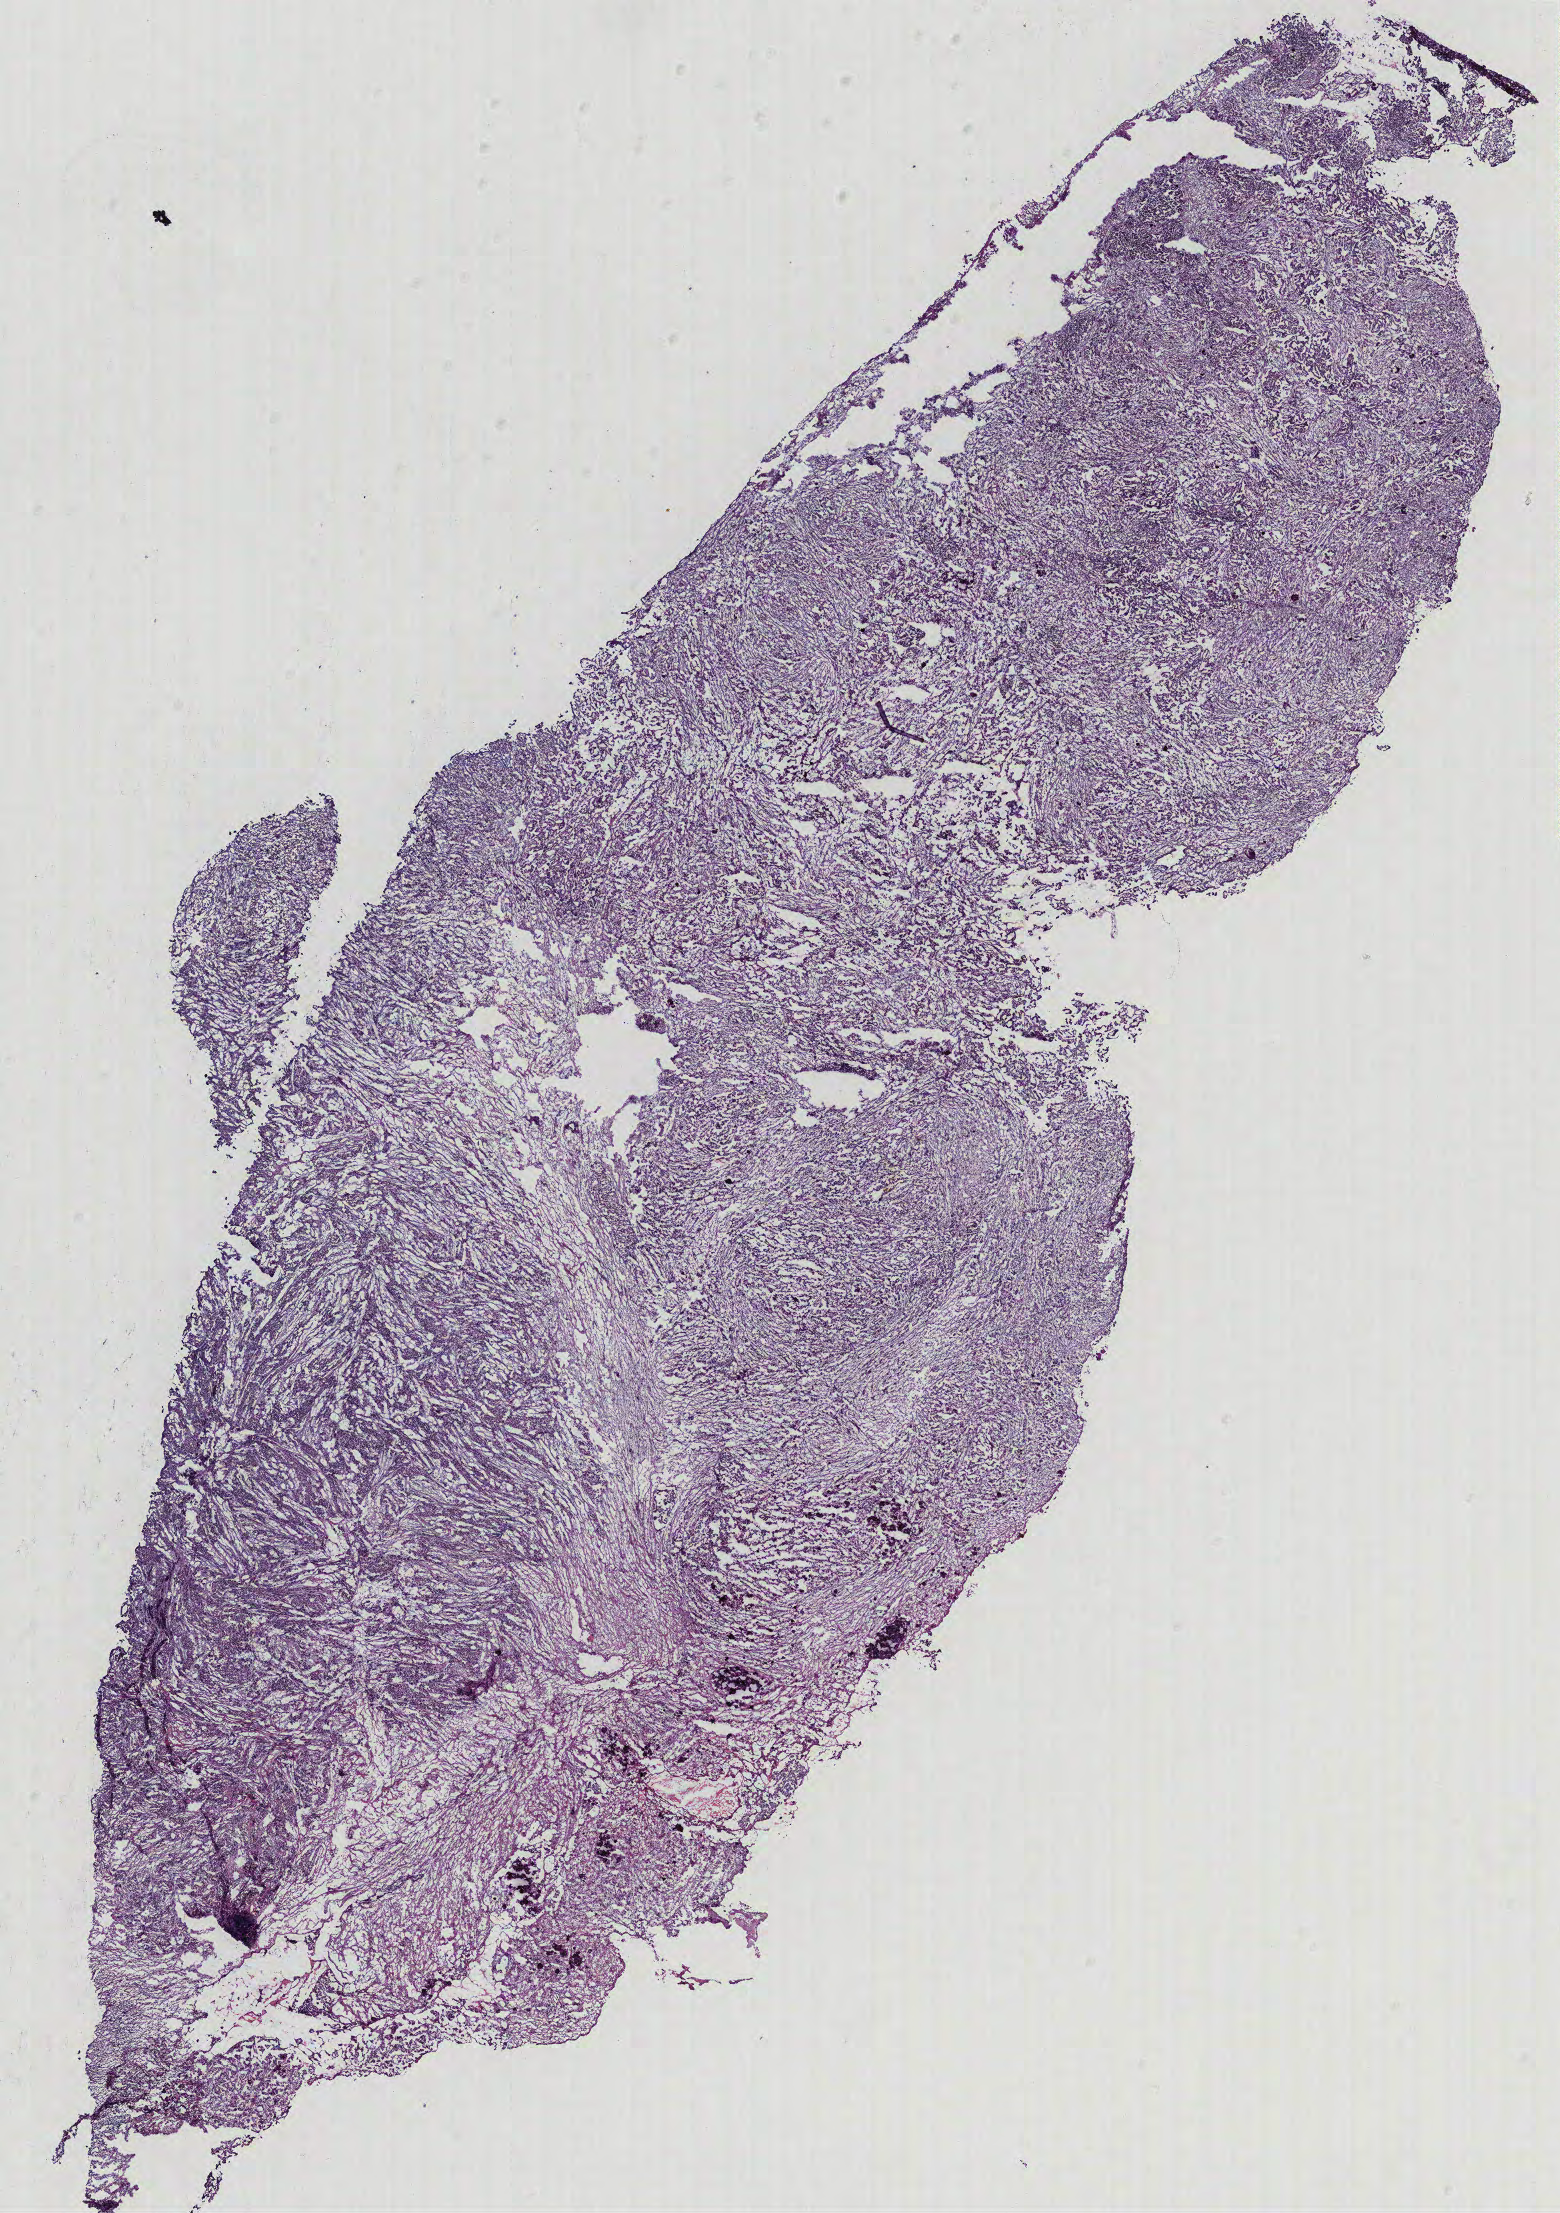
H&E-stained whole-slide image — whole scanned area (about 12.5 x 17.7 mm) shown as a low-resolution overview. Ovary, tissue type not recorded.
Patient diagnosis (cohort enrolment): ovarian cancer (ovary).